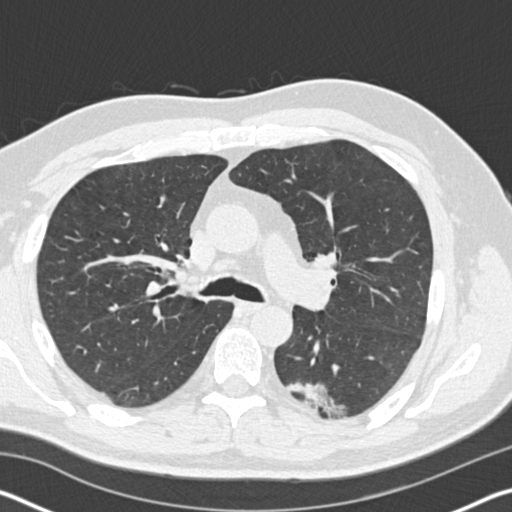
Low-dose screening chest CT, one axial slice. Position 111 of 178 along the scan axis. Reconstruction kernel B30f. 120 kVp. Lung window (W 1500 / L -600 HU). 512 × 512 image matrix.
Annotated regions visible in this slice (expert manual segmentation):
- lesion 1 (tumor, lower lobe of left lung): box from (x=288, y=382) to (x=344, y=417) px